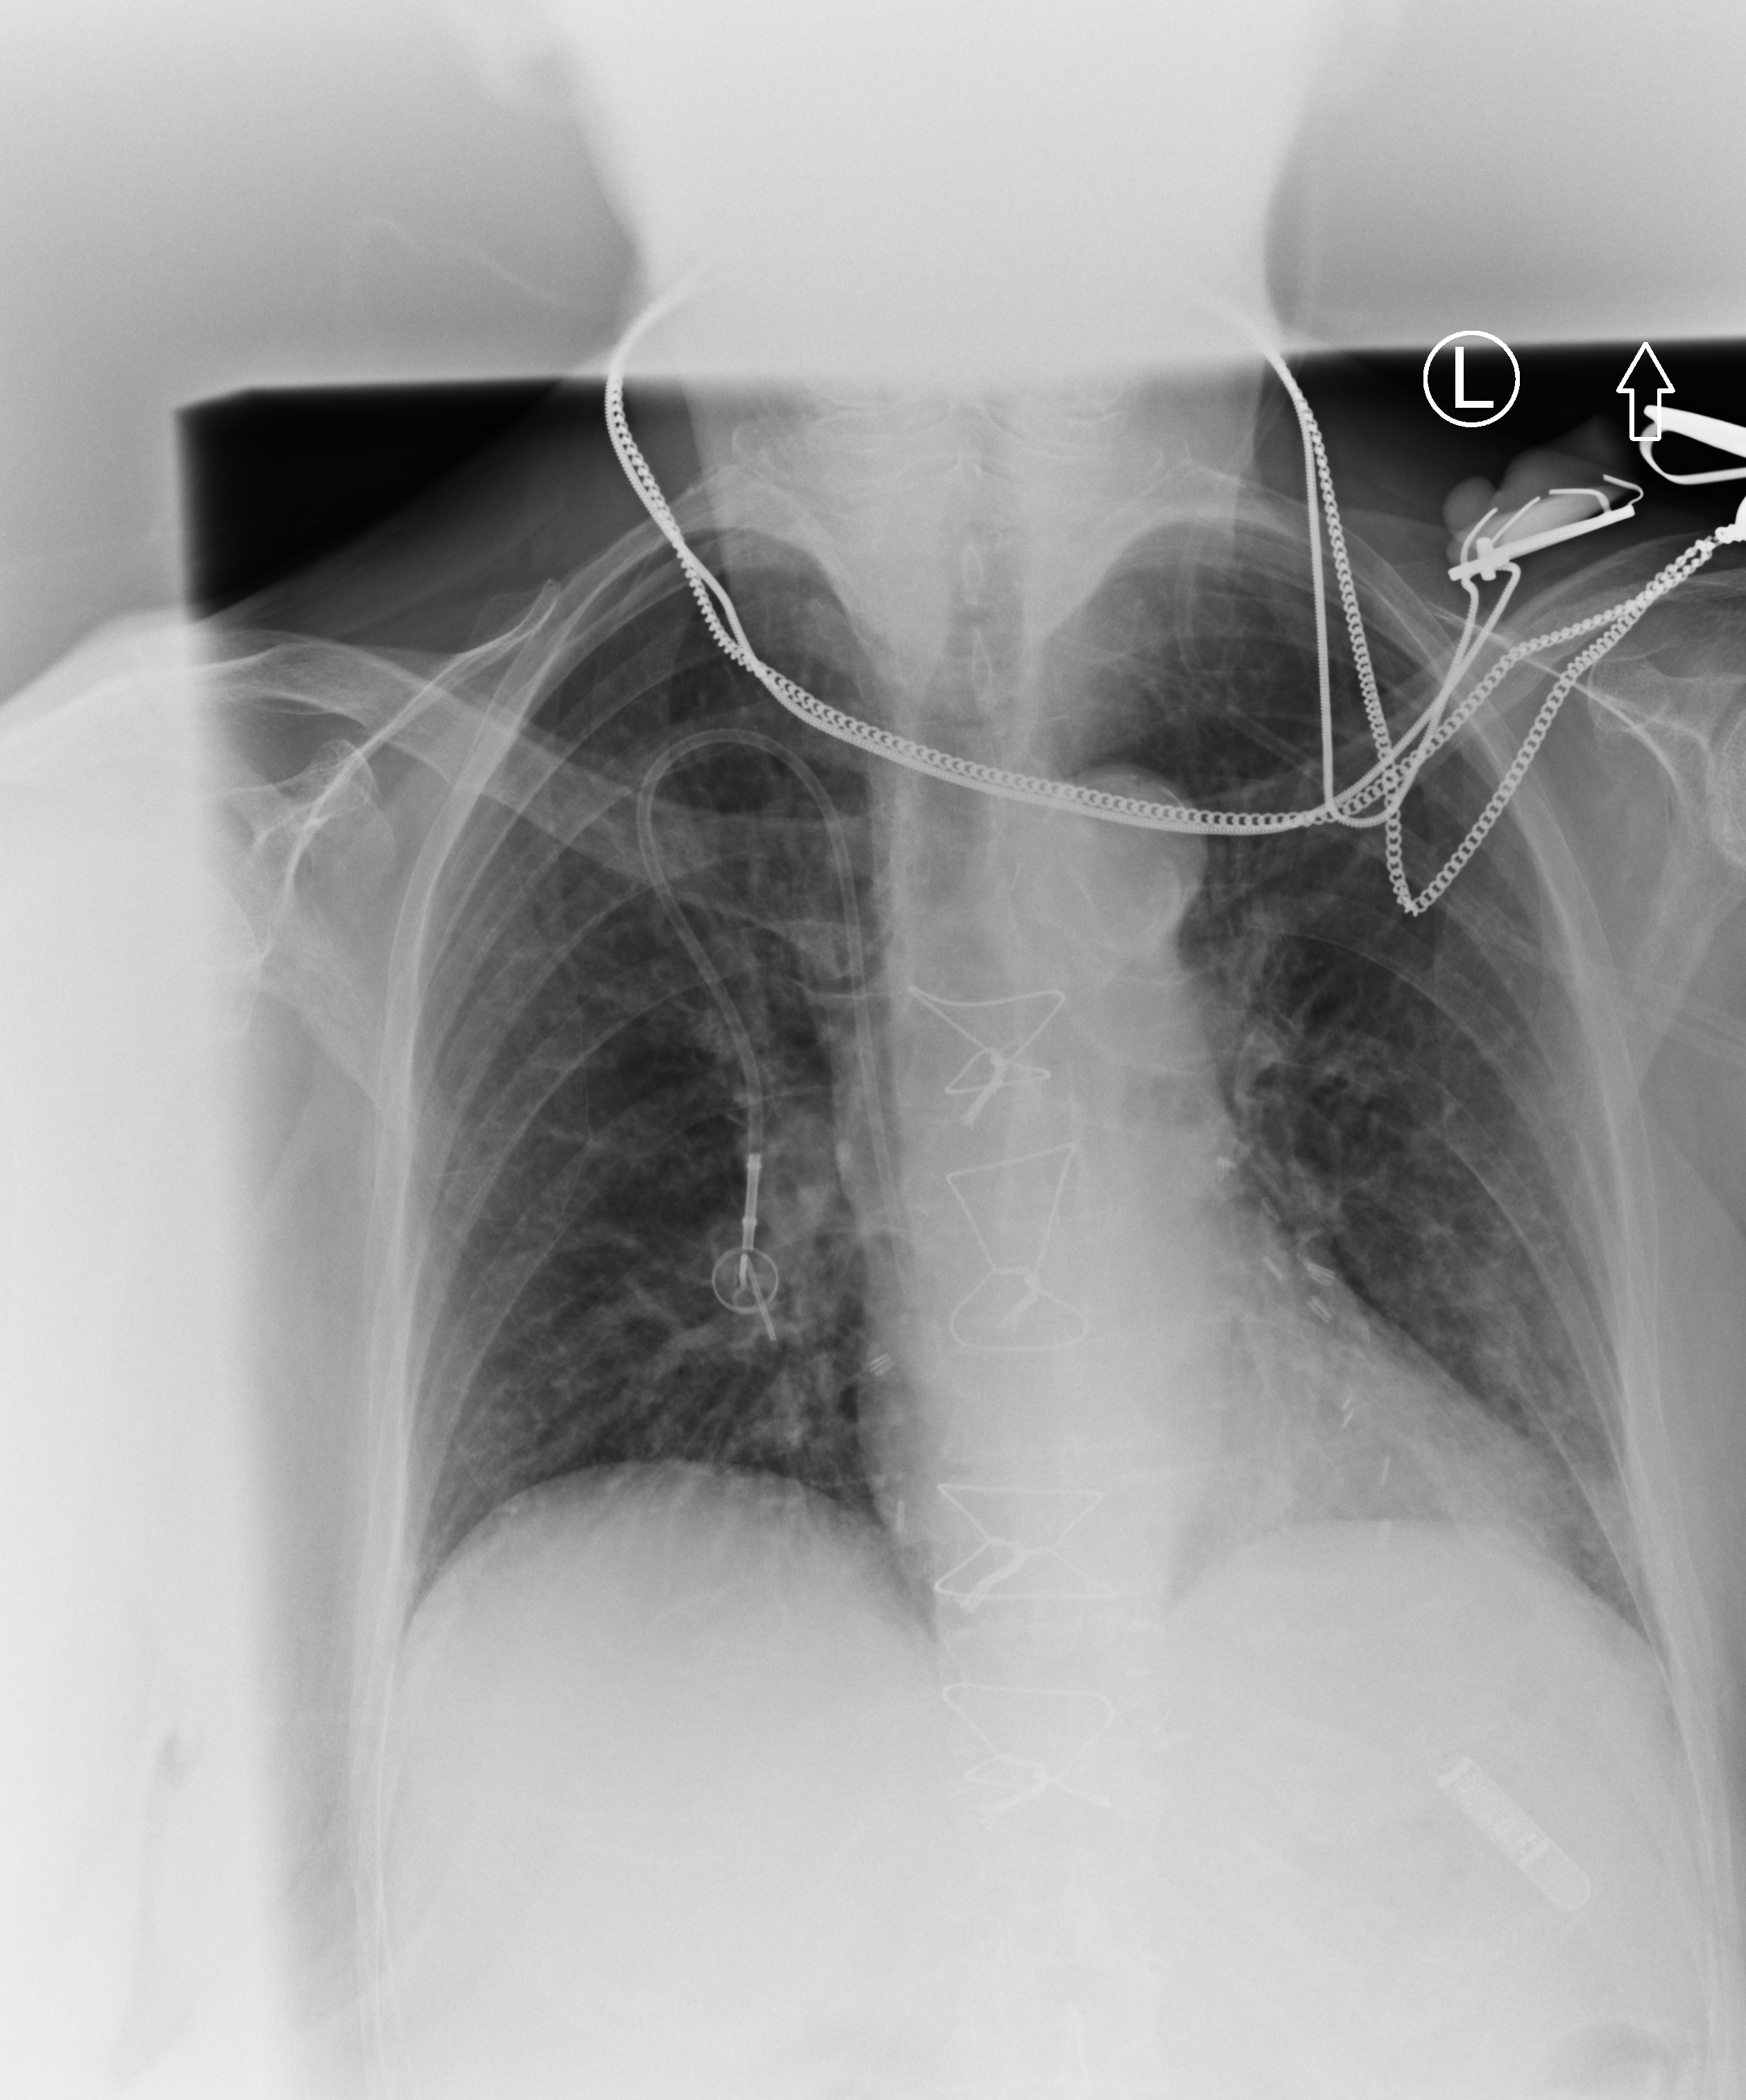
Chest X-ray (portable); anteroposterior (AP) projection. Patient hospitalised with COVID-19; female, aged 75–90 years.
Hospital-stay facts (about this admission, not read from this image; timing relative to this image not recorded): chronic kidney disease (admission record): no; length of hospital stay: 7 days.